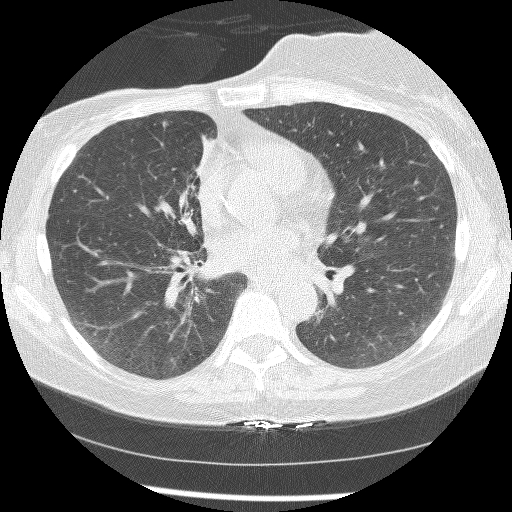
Low-dose screening chest CT, axial slice, baseline annual screen, lung window (W 1500 / L -600 HU), 2.5 mm slice thickness, lung (sharp) reconstruction kernel (BONE), 120 kVp, slice 78 of 172 in the series. Female, age 56 years at enrolment. Current smoker at enrolment.
• Expert reader's lesion annotation, bounding box (x1, y1, x2, y2) in pixels: (147, 109, 180, 142).
• The screening reader recorded 2 non-calcified nodules or masses ≥4 mm on this exam; which of them this box marks is not recorded.
• Participant outcome: lung cancer diagnosed 1185 days after this screen (after the third annual screen) — adenocarcinoma, NOS, right upper lobe, stage IIIB (AJCC 6th edition), 8 mm at pathology.